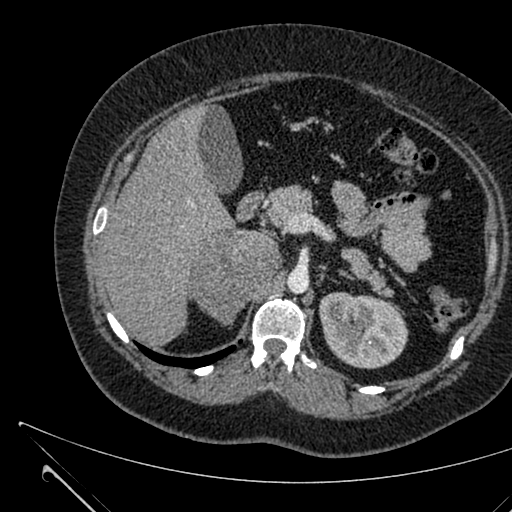
Contrast-enhanced abdominal CT, one axial slice. Position 415 of 731 along the scan axis. 120 kVp. Intravenous contrast given. Soft-tissue window (W 400 / L 40 HU). 1 mm slice thickness. 512 × 512 image matrix. Patient: female, 36 years. Case-level facts recorded for this patient, not image findings: diagnosis: adrenocortical carcinoma; tumour side: right adrenal; tumour size at pathology: 10 cm; Ki-67 index: 20 %; stage (as recorded): 4.
Outlined on this slice (semi-automatic segmentation, software-assisted and operator-edited):
- mass: bounding box [x1, y1, x2, y2] px = [193, 232, 279, 323]